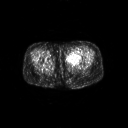
FDG PET of an extremity soft-tissue mass (from a PET/CT study), one axial slice. Slice 17 of 267 in the series (ordered by position). 3.27 mm slice thickness. 128 × 128 image matrix, field of view 700 × 700 mm. Female patient, age 47 years. From the clinical record (not read from this slice): histological type: myxofibrosarcoma; grade: intermediate; site of the primary tumour: left thigh.
Annotated regions visible in this slice (expert contour drawn on MRI and transferred to this co-registered scan by the dataset authors):
- gross tumour volume including surrounding oedema: bounding box (x1, y1, x2, y2) in pixels: (67, 53, 81, 63)
- gross tumour volume (mass): (68, 53, 80, 63)